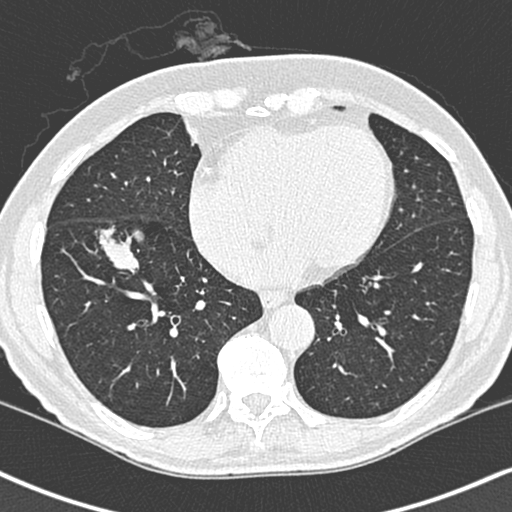
Low-dose screening chest CT, one axial slice; position 100 of 248 along the scan axis; lung window (W 1500 / L -600 HU); 1.3 mm slice thickness; 512 × 512 image matrix, field of view 323 × 323 mm.
Annotated regions visible in this slice (manually delineated by an expert):
- lesion 1 (tumor, lower lobe of right lung): bounding box <99,187,143,233> (left, top, right, bottom; pixels)